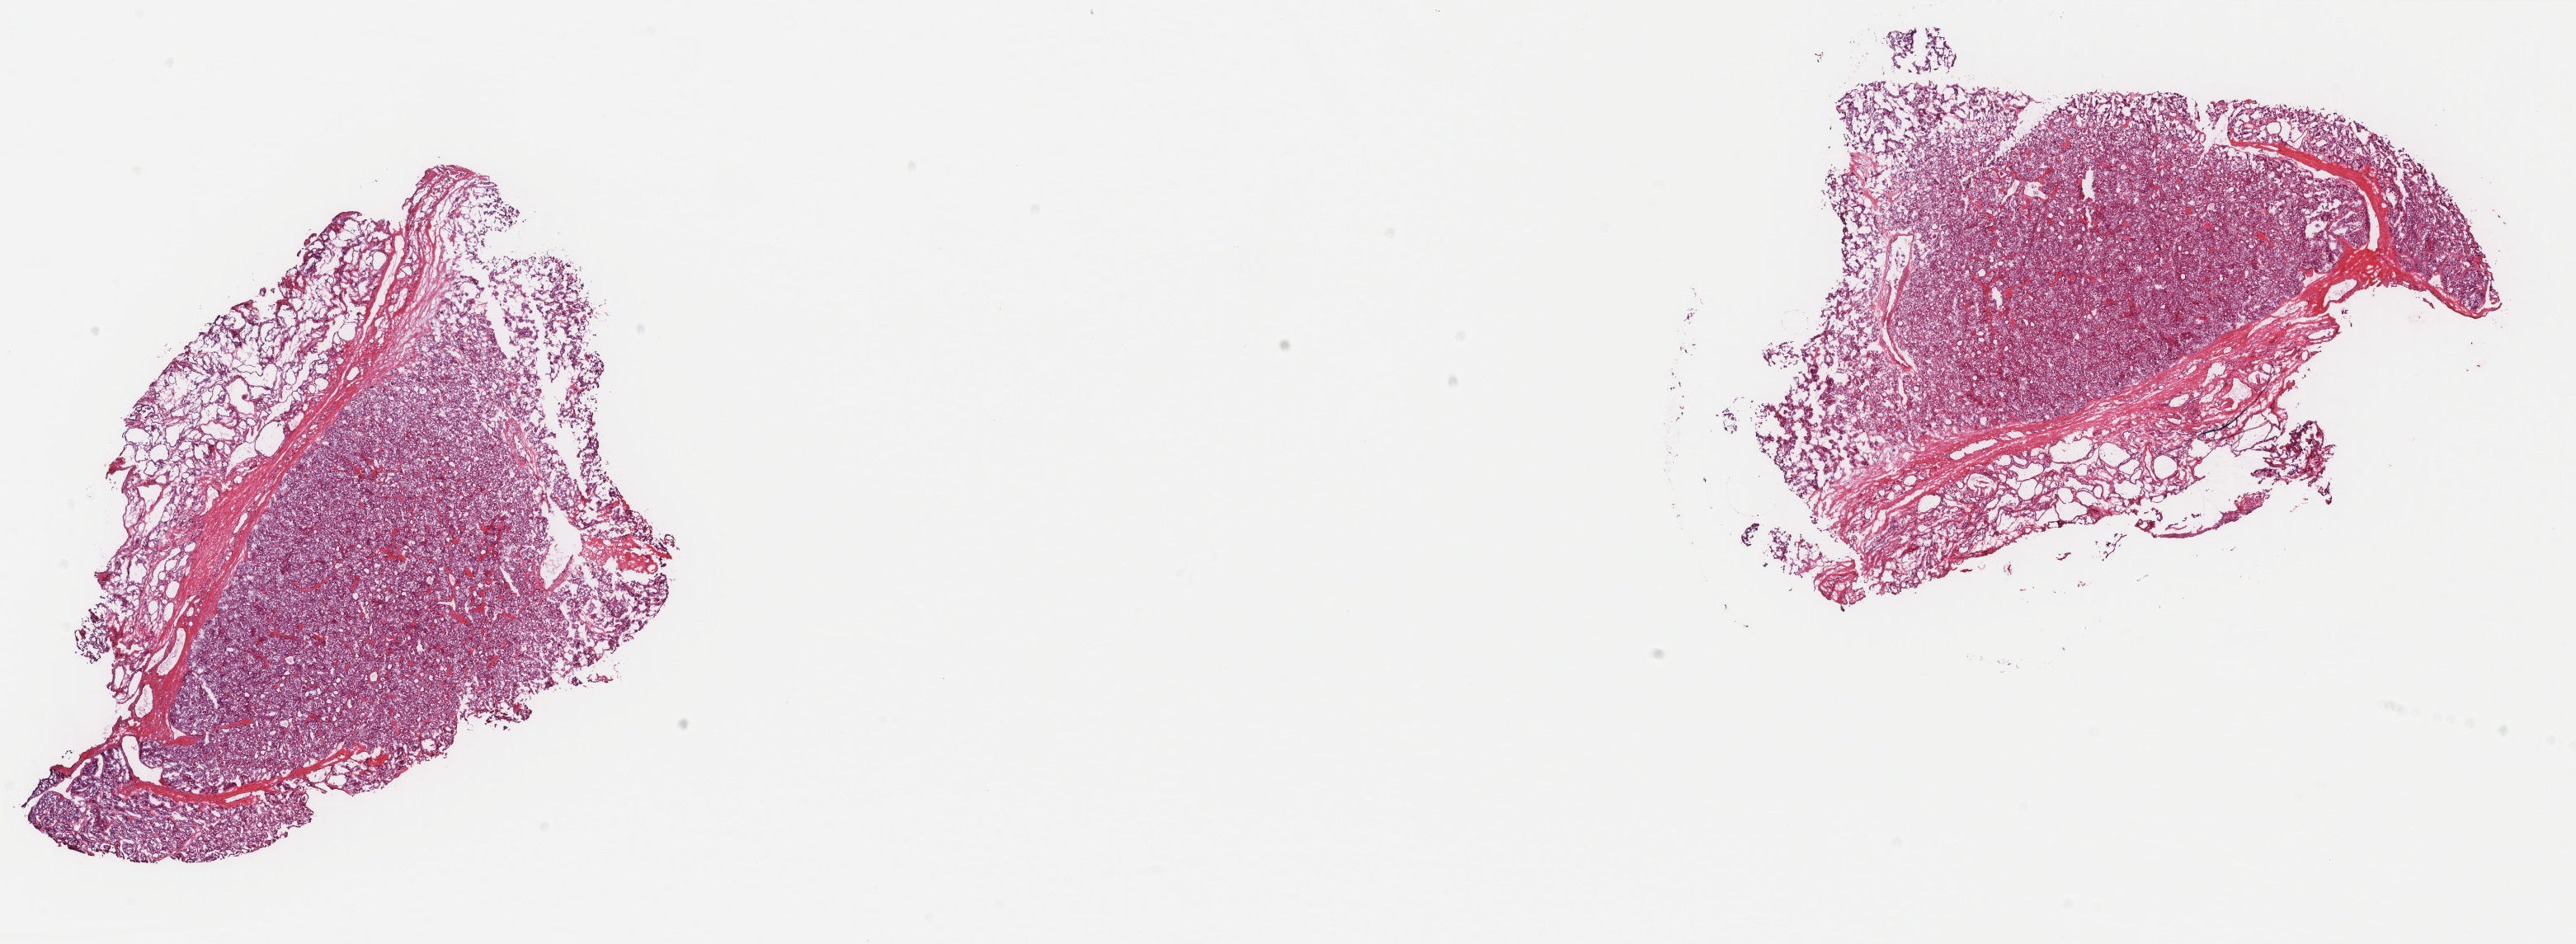
Digitized H&E-stained tissue section (whole slide), low-resolution overview of the scanned area, about 24.8 x 9.1 mm (from a 40x scan), frozen section from the top of the tissue portion, thyroid, primary tumour sample. Male, age 46 years at initial diagnosis. Composition of this section per pathologist review: tumour cells 75%, tumour nuclei 75%, normal cells 10%, stromal cells 15%, necrosis 0%. Infiltration values recorded for this section: lymphocyte infiltration 1%, monocyte infiltration 0%, neutrophil infiltration 0%.
• AJCC pathologic stage: III (7th edition)
• TNM: T3 N0 MX
• diagnosis: Papillary carcinoma, follicular variant (thyroid gland)
• lymph nodes positive (case pathology): 0 of 5 examined
• laterality: right